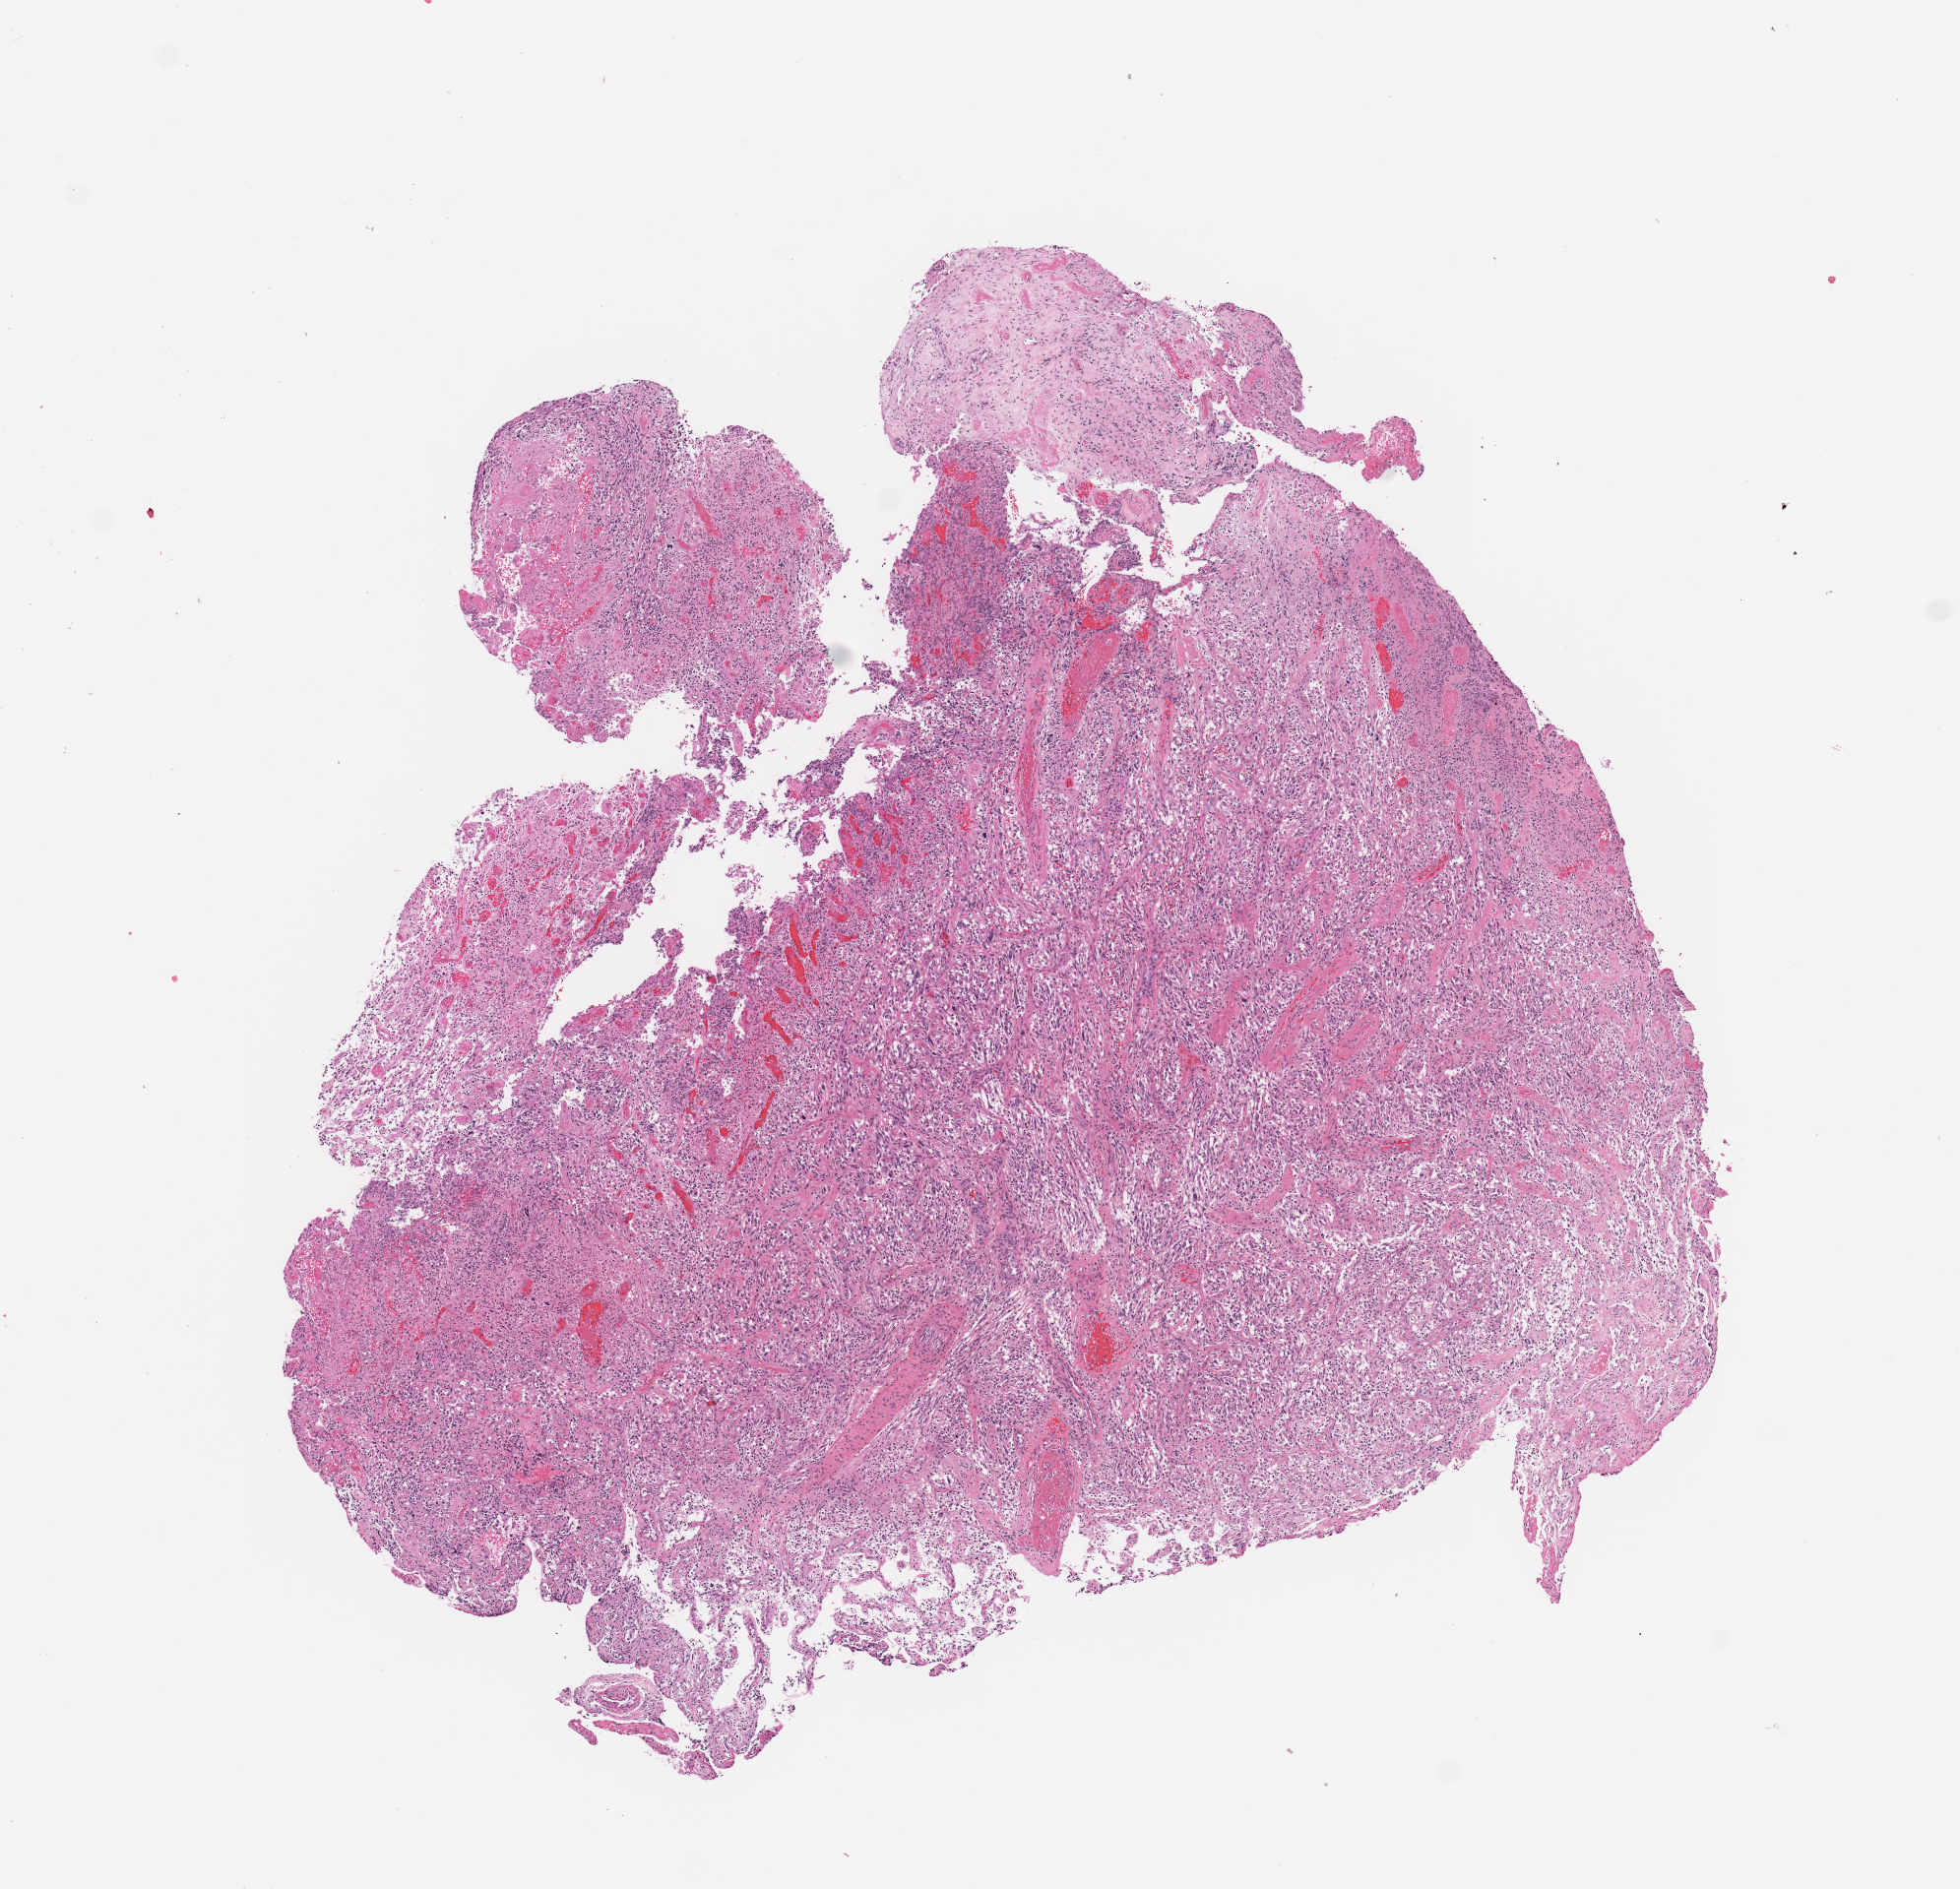
H&E whole-slide image, a low-resolution overview of the entire scanned area, about 7.9 x 7.6 mm (acquisition: 20x scan). Tumour tissue sample, sampled site: brain. 59-year-old male patient. Pathologist review of this section (percent, as recorded): tumour nuclei 70%, necrosis 10%.
Diagnosis: Glioblastoma.